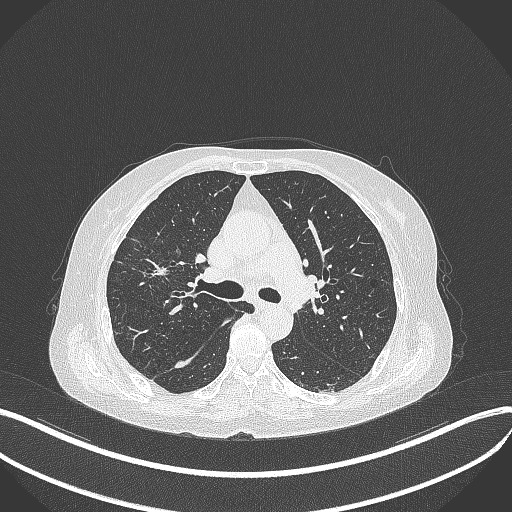
Chest CT, one axial slice. Slice 256 of 429 in the series (ordered by position). Reconstruction kernel B70f. Lung window (W 1500 / L -600 HU). 512 × 512 image matrix, field of view 400 × 400 mm. Patient: female, 69 years. Case-level facts recorded for this patient, not image findings: clinical TNM (as recorded): T1b N3 M0.
Annotated regions visible in this slice (bounding box drawn by a radiologist):
- lung tumour (recorded histology: small cell carcinoma): box from (x=136, y=255) to (x=175, y=286) px